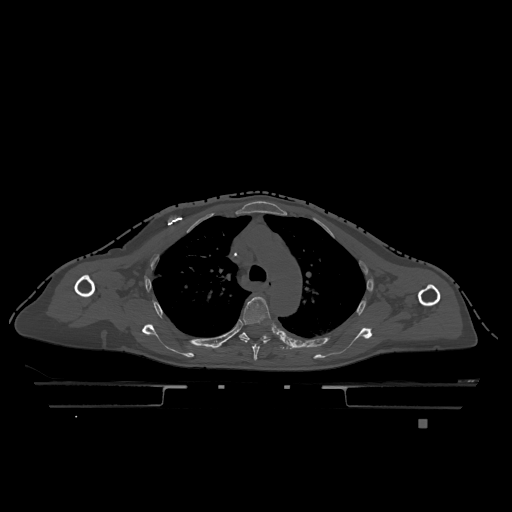
CT including the spine, one axial slice; position 864 of 1317 along the scan axis; bone window (W 1800 / L 400 HU); 512 × 512 image matrix. Female patient, age 74 years. From the clinical record (not read from this slice): primary cancer: lung; vertebrae with lytic lesions (as recorded): T1, T4, T5, T6, L4, L5.
Outlined on this slice (semi-automatically segmented with operator editing):
- T4 vertebra: bounding box [x1, y1, x2, y2] px = [239, 297, 272, 361]
- T5 vertebra: [239, 332, 285, 350]